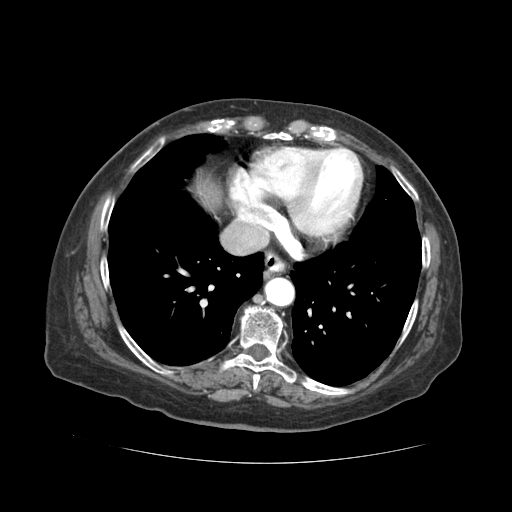
Contrast-enhanced abdominal CT (liver protocol), one axial slice; slice 49 of 59 in the series (ordered by position); reconstruction kernel STANDARD; soft-tissue window (W 400 / L 40 HU); 2.5 mm slice thickness; 512 × 512 image matrix. Case-level facts recorded for this patient, not image findings: diagnosis: hepatocellular carcinoma (patient treated with transarterial chemoembolisation; whether this scan precedes or follows treatment is not stated here); TNM stage (as recorded): Stage-I.
Annotated regions visible in this slice (semi-automatically segmented with operator editing):
- liver parenchyma outside the tumour (the mass and vessels are separate outlines, so this box may not span the whole liver): box from (x=196, y=180) to (x=220, y=209) px